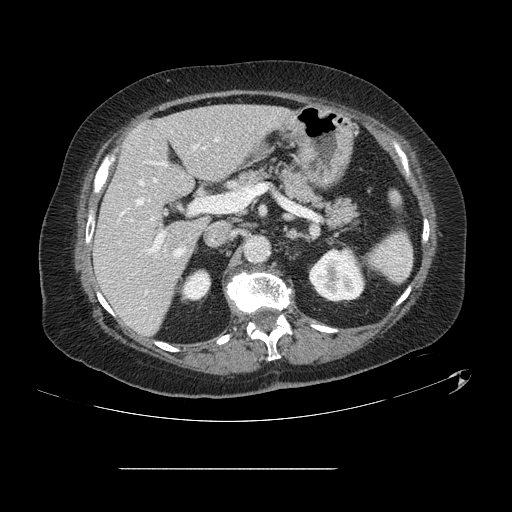
Contrast-enhanced abdominal CT, one axial slice; slice 69 of 148 in the series (ordered by position); 120 kVp; intravenous contrast given; soft-tissue window (W 400 / L 40 HU); 2.5 mm slice thickness; 512 × 512 image matrix. Female patient, age 75 years. From the clinical record (not read from this slice): diagnosis: colorectal cancer liver metastases, imaged before liver resection; multiple liver metastases: no; largest metastasis: 2.4 cm; disease in both lobes: no.
Structures marked on this image (expert manual segmentation):
- hepatic veins: bounding box <122,138,218,256> (left, top, right, bottom; pixels)
- liver: <95,105,288,334>
- planned liver remnant (the part of the liver to remain after resection): <95,105,288,334>
- portal vein (with intrahepatic branches): <132,147,209,254>